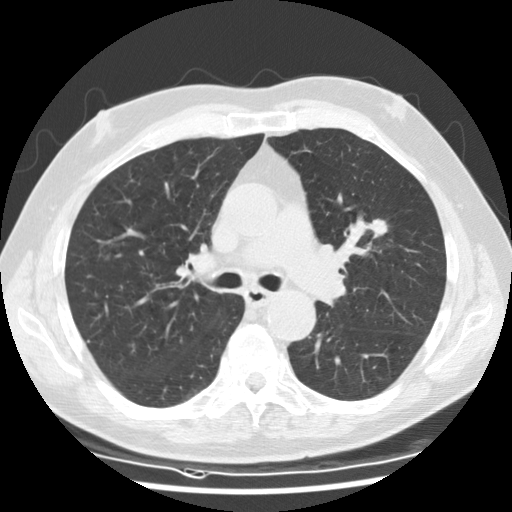
Low-dose screening chest CT, one axial slice. Position 79 of 135 along the scan axis. Reconstruction kernel STANDARD. 120 kVp. Lung window (W 1500 / L -600 HU). 2.5 mm slice thickness. 512 × 512 image matrix, field of view 340 × 340 mm.
Outlined on this slice (outlined manually by an expert reader):
- lesion 1 (tumor, upper lobe of left lung): box from (x=369, y=219) to (x=388, y=239) px